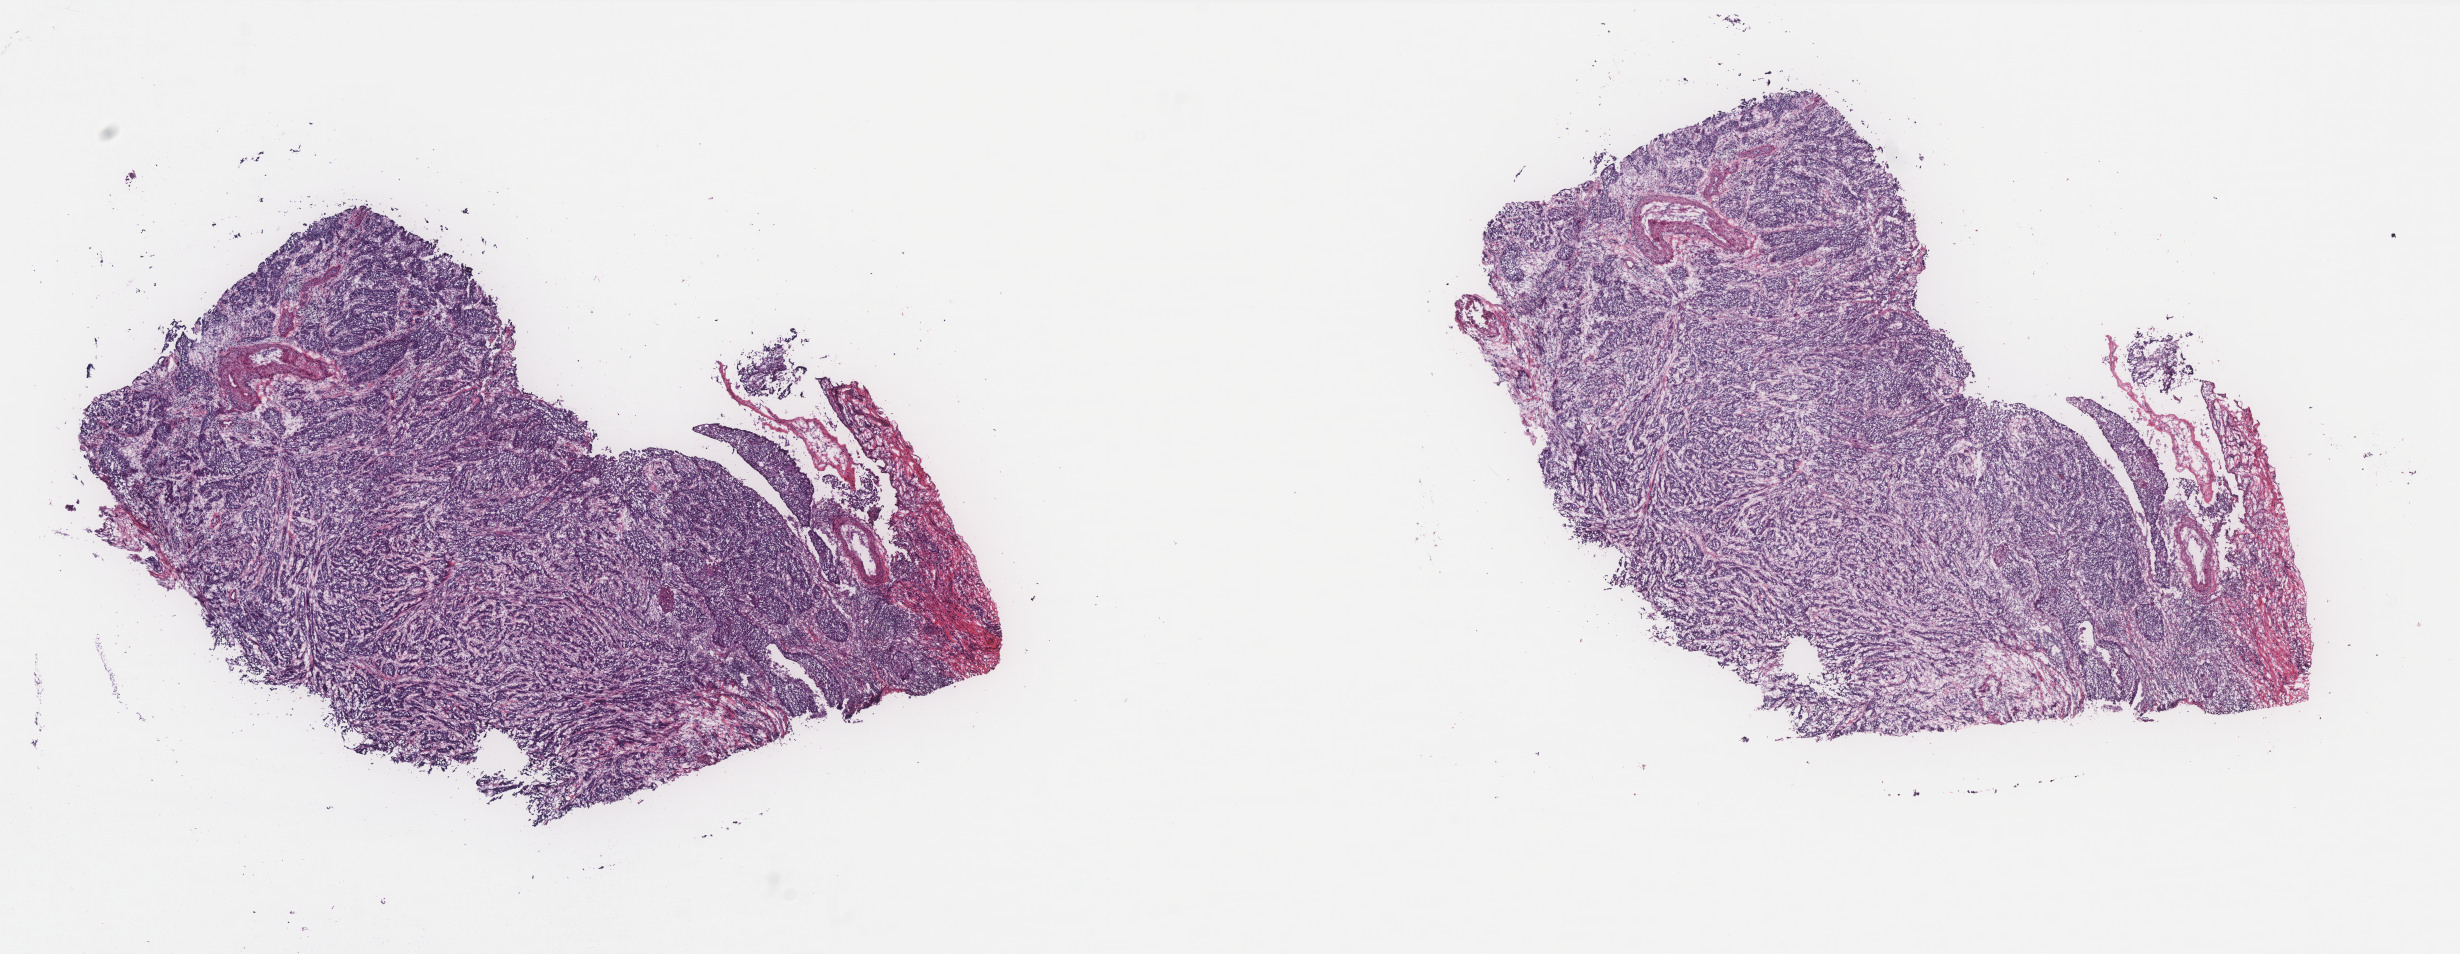
H&E-stained whole-slide image, a low-resolution overview of the entire scanned area, about 19.7 x 7.6 mm; frozen section; sample: primary tumour, cervix. Female, age 51 years at initial diagnosis. Histologic grade: G3 (poorly differentiated). Pathologist review of this section (percent, as recorded): tumour cells 100%, tumour nuclei 75%, normal cells 0%, stromal cells 0%, necrosis 0%. Inflammatory infiltration, as recorded: lymphocyte infiltration 0%, monocyte infiltration 0%, neutrophil infiltration 0%.
Histologic diagnosis: Squamous cell carcinoma, NOS.